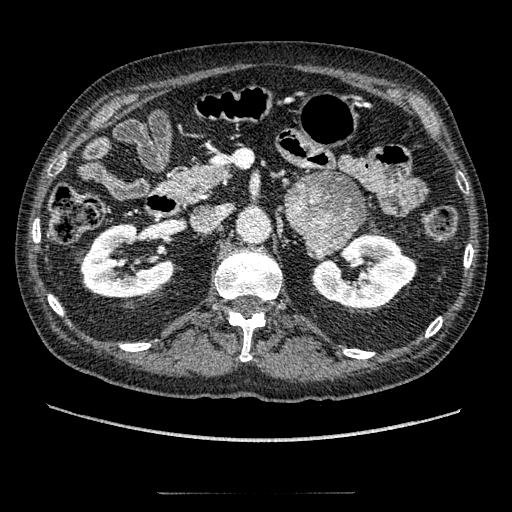
Contrast-enhanced abdominal CT, one axial slice; slice 106 of 274 in the series (ordered by position); intravenous contrast given; soft-tissue window (W 400 / L 40 HU); 512 × 512 image matrix, field of view 381 × 381 mm. Patient: male, 69 years. Case-level facts recorded for this patient, not image findings: diagnosis: adrenocortical carcinoma; tumour side: left adrenal.
Outlined on this slice (semi-automatic segmentation, software-assisted and operator-edited):
- mass: bounding box <287,173,366,257> (left, top, right, bottom; pixels)